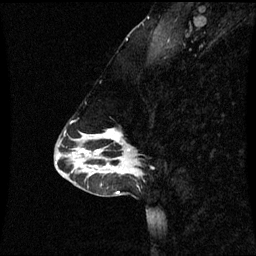
Breast MRI (dynamic contrast-enhanced), one sagittal slice. Position 23 of 60 along the scan axis. Dynamic contrast-enhanced series, image 2 of 3 at this slice position (ordered by acquisition). 1.5 T. TE 4.2 ms, TR 8.9 ms. 256 × 256 image matrix, field of view 220 × 220 mm. Female patient, age 43 years. Case-level facts recorded for this patient, not image findings: setting: breast cancer imaged before/during neoadjuvant chemotherapy; receptor status: HR-positive, HER2-negative.
Outlined on this slice (semi-automatically segmented with operator editing):
- analysis volume of interest (the breast-tissue region the enhancement analysis was run in; not a lesion): bounding box <84,130,140,171> (left, top, right, bottom; pixels)
- tumour enhancement mask (voxels above the 70 % enhancement threshold inside the analysis volume of interest): <104,130,129,151>